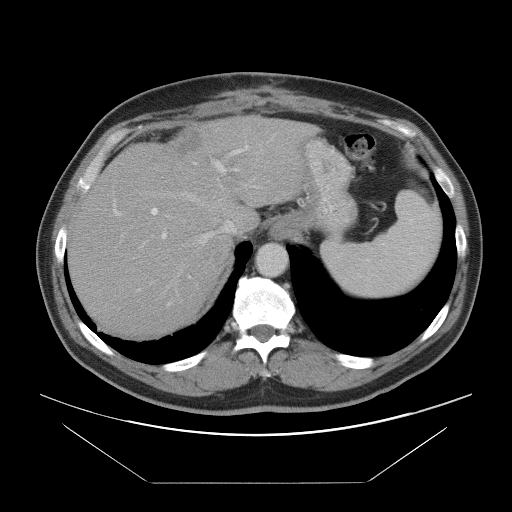
Contrast-enhanced abdominal CT, one axial slice. Slice 70 of 97 in the series (ordered by position). Intravenous contrast given. Soft-tissue window (W 400 / L 40 HU). 5 mm slice thickness. 512 × 512 image matrix. Male patient, age 62 years. From the clinical record (not read from this slice): diagnosis: colorectal cancer liver metastases, imaged before liver resection; multiple liver metastases: no; largest metastasis: 7 cm; chemotherapy before resection: yes.
Annotated regions visible in this slice (outlined manually by an expert reader):
- hepatic veins: box from (x=152, y=139) to (x=287, y=288) px
- liver: (x=70, y=117)–(x=306, y=335)
- planned liver remnant (the part of the liver to remain after resection): (x=70, y=171)–(x=231, y=335)
- portal vein (with intrahepatic branches): (x=113, y=145)–(x=257, y=291)
- liver metastasis: (x=168, y=131)–(x=202, y=159)